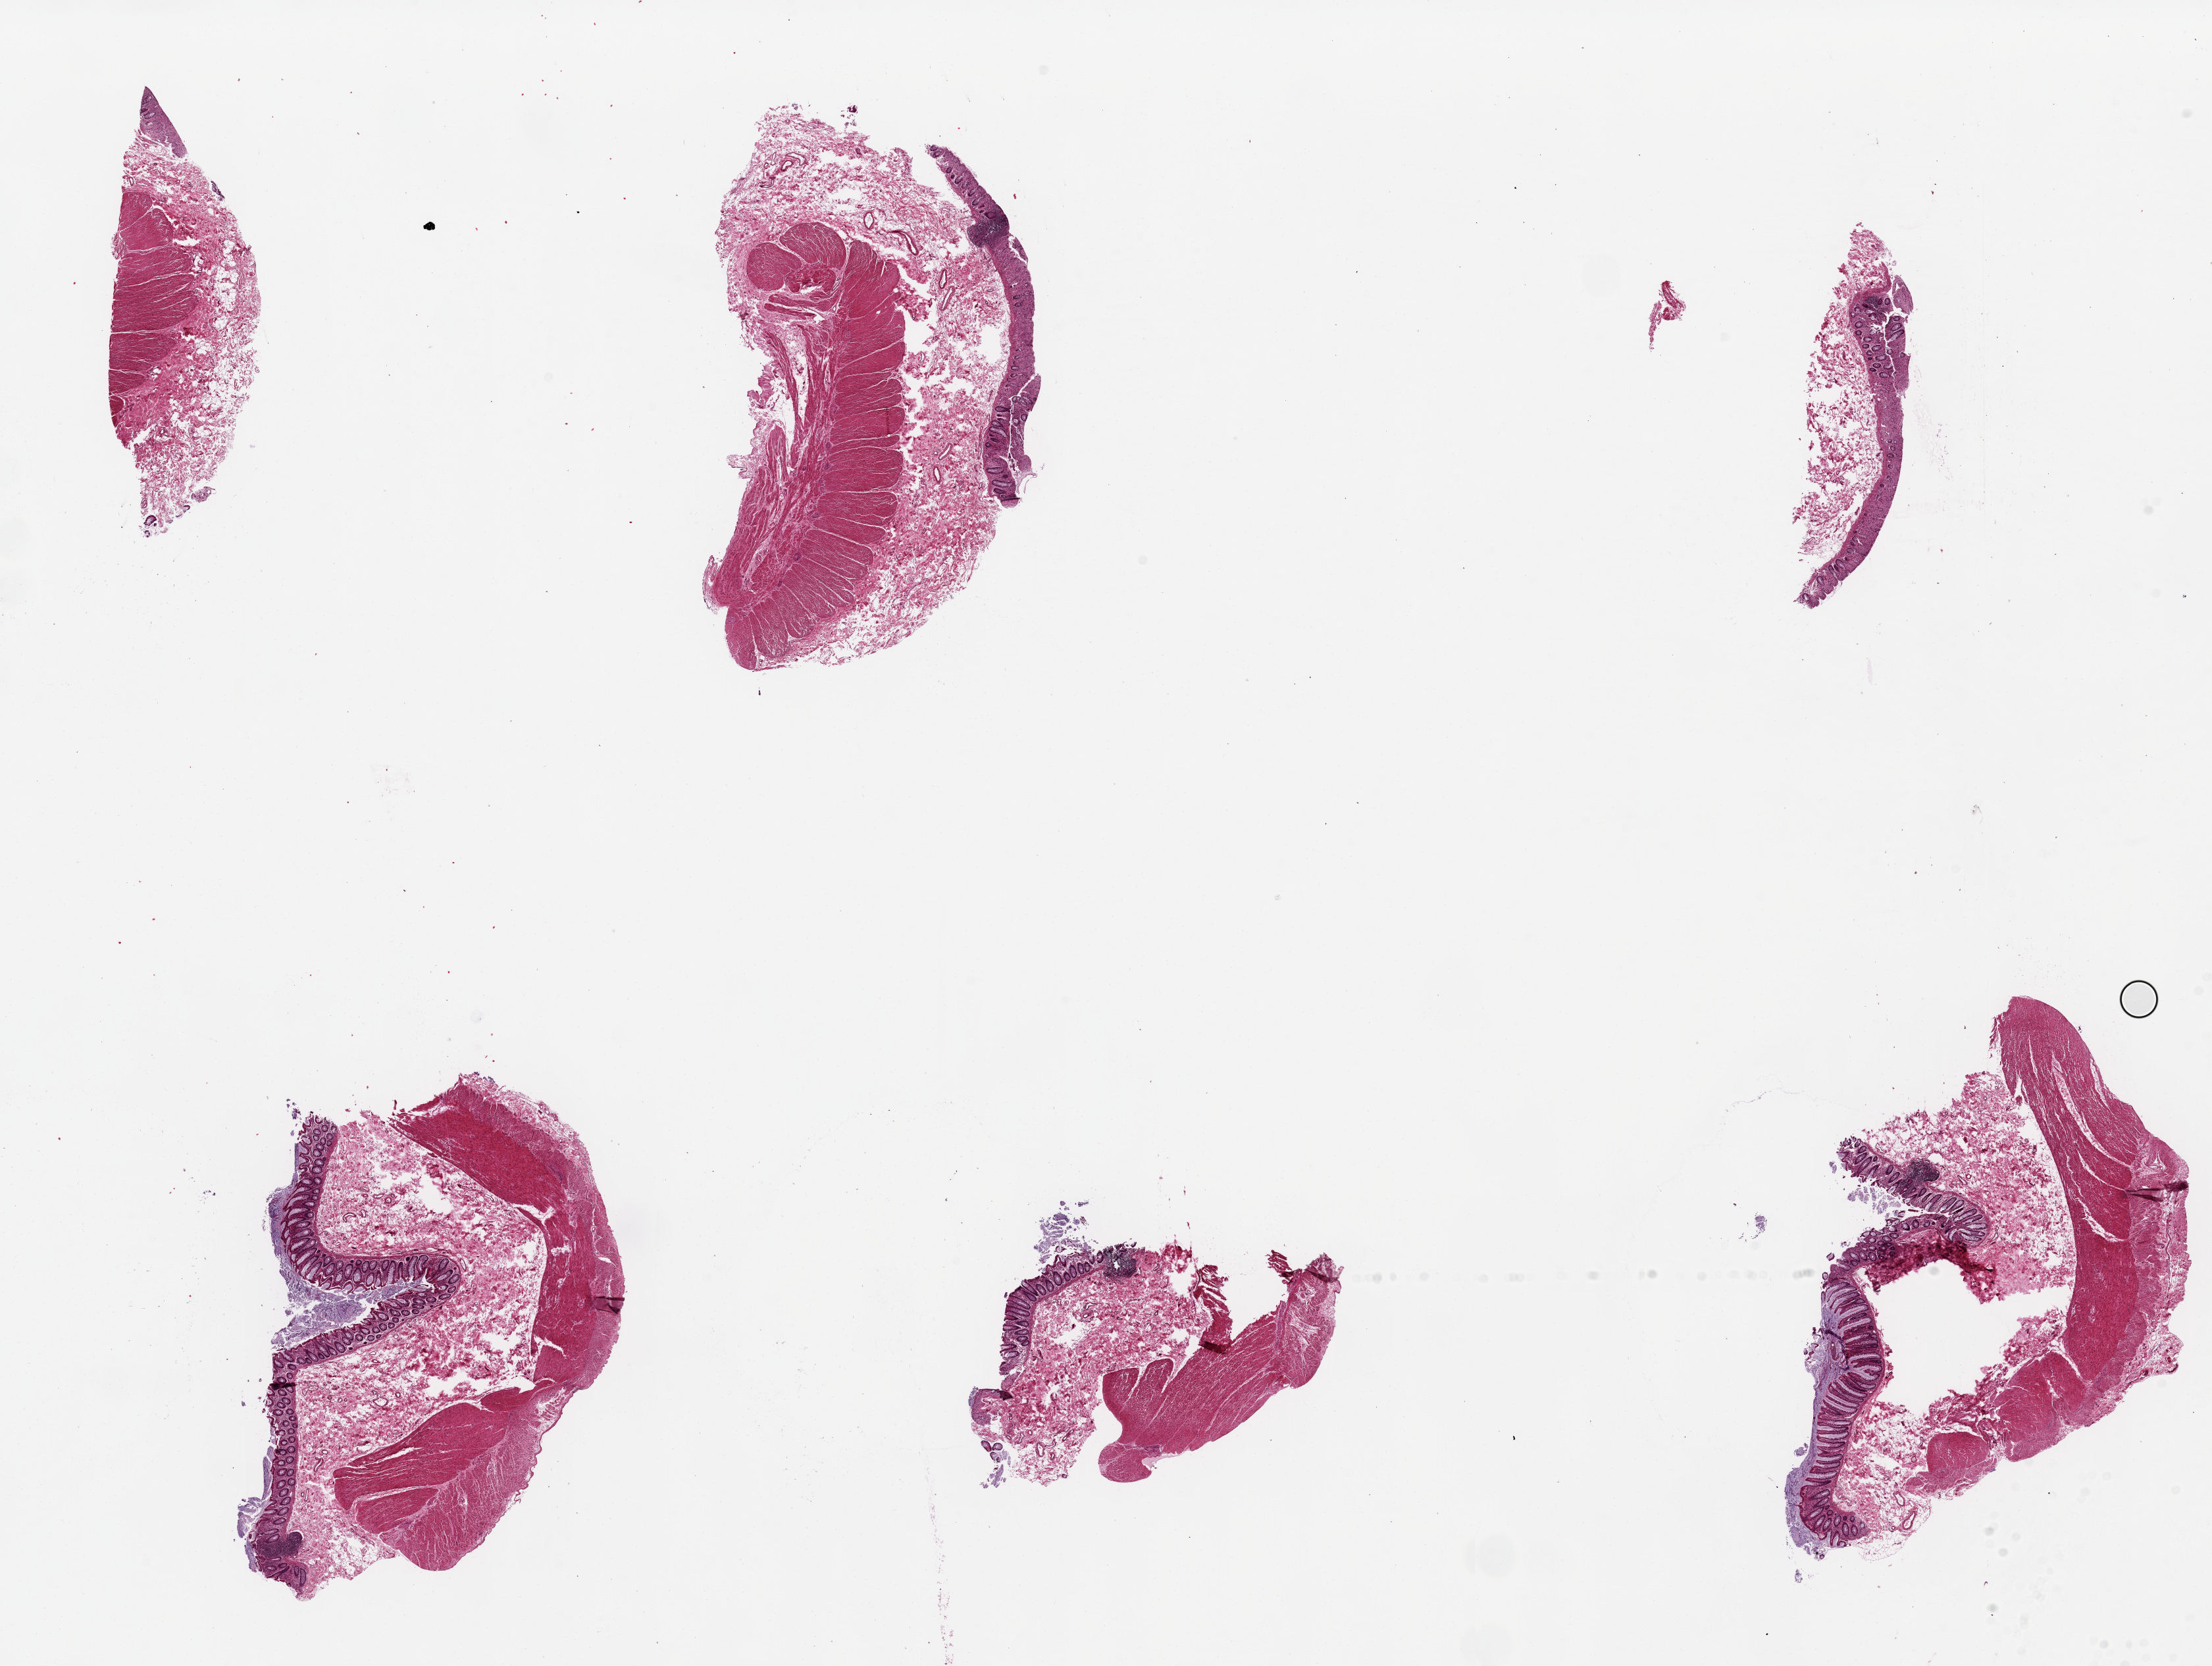
Digitized H&E-stained section — shown as a low-resolution overview of the whole scanned area (about 26.6 x 20.0 mm); PAXgene-fixed paraffin-embedded (PFPE) section; section of sigmoid colon (target tissue); tissue donor sample. Male donor.
Review note (as recorded): 6 pieces, ~7x4mm, up to ~50% muscularis in 5 sections, one with no muscle.